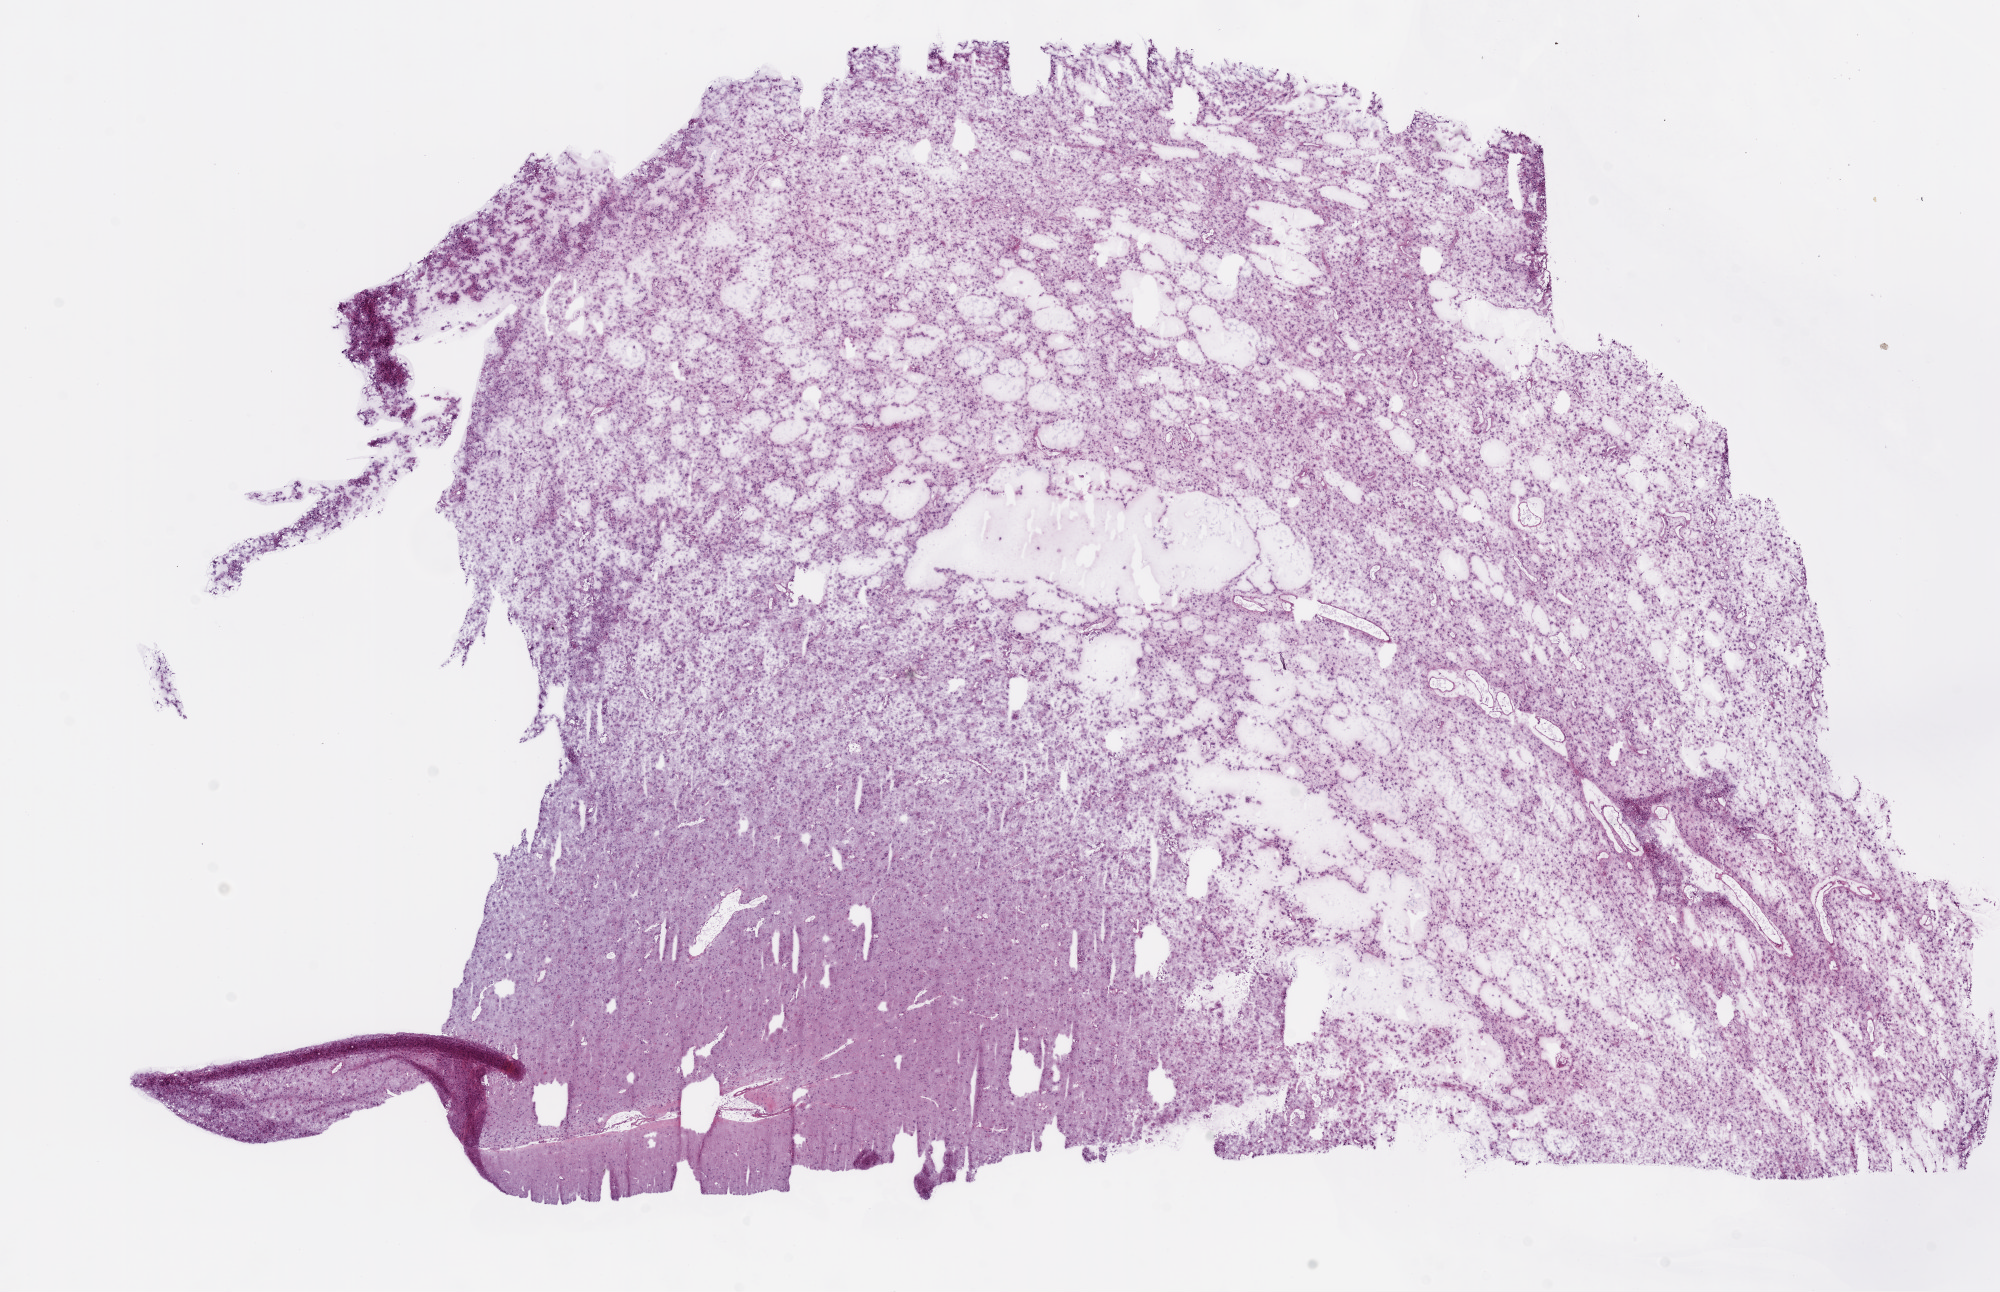
Whole-slide histology image, Hematoxylin and eosin (H&E) stained — shown as a low-resolution overview of the whole scanned area (about 16.0 x 10.4 mm, slide scanned at 20x), frozen section from the top of the tissue portion, primary tumour sample from the brain. Patient: male, age at initial diagnosis 61 years. Histologic grade: G3 (poorly differentiated). Composition of this section per pathologist review: tumour cells 100%, tumour nuclei 80%, normal cells 0%, stromal cells 0%, necrosis 0%.
Diagnosis: Mixed glioma (cerebrum).